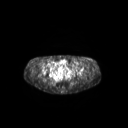
FDG PET of an extremity soft-tissue mass (from a PET/CT study), one axial slice; position 81 of 267 along the scan axis; 128 × 128 image matrix, field of view 600 × 600 mm. Female patient, age 24 years. Case-level facts recorded for this patient, not image findings: histological type: leiomyosarcoma; grade: high; site of the primary tumour: groin.
Annotated regions visible in this slice (expert contour drawn on MRI and transferred to this co-registered scan by the dataset authors):
- gross tumour volume including surrounding oedema: box from (x=79, y=60) to (x=89, y=64) px